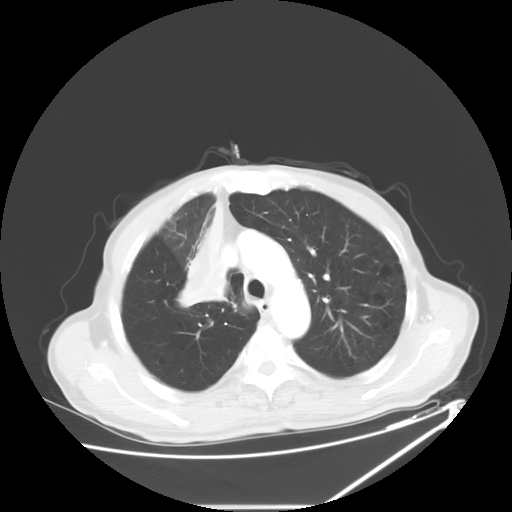
Chest CT, one axial slice; slice 45 of 60 in the series (ordered by position); reconstruction kernel STANDARD; lung window (W 1500 / L -600 HU); 5 mm slice thickness; 512 × 512 image matrix, field of view 410 × 410 mm. Patient: male, 73 years. From the clinical record (not read from this slice): clinical TNM (as recorded): T2a N1 M0.
Structures marked on this image (rectangle marked by the reading radiologist):
- lung tumour (recorded histology: squamous cell carcinoma): bounding box <181,191,228,320> (left, top, right, bottom; pixels)